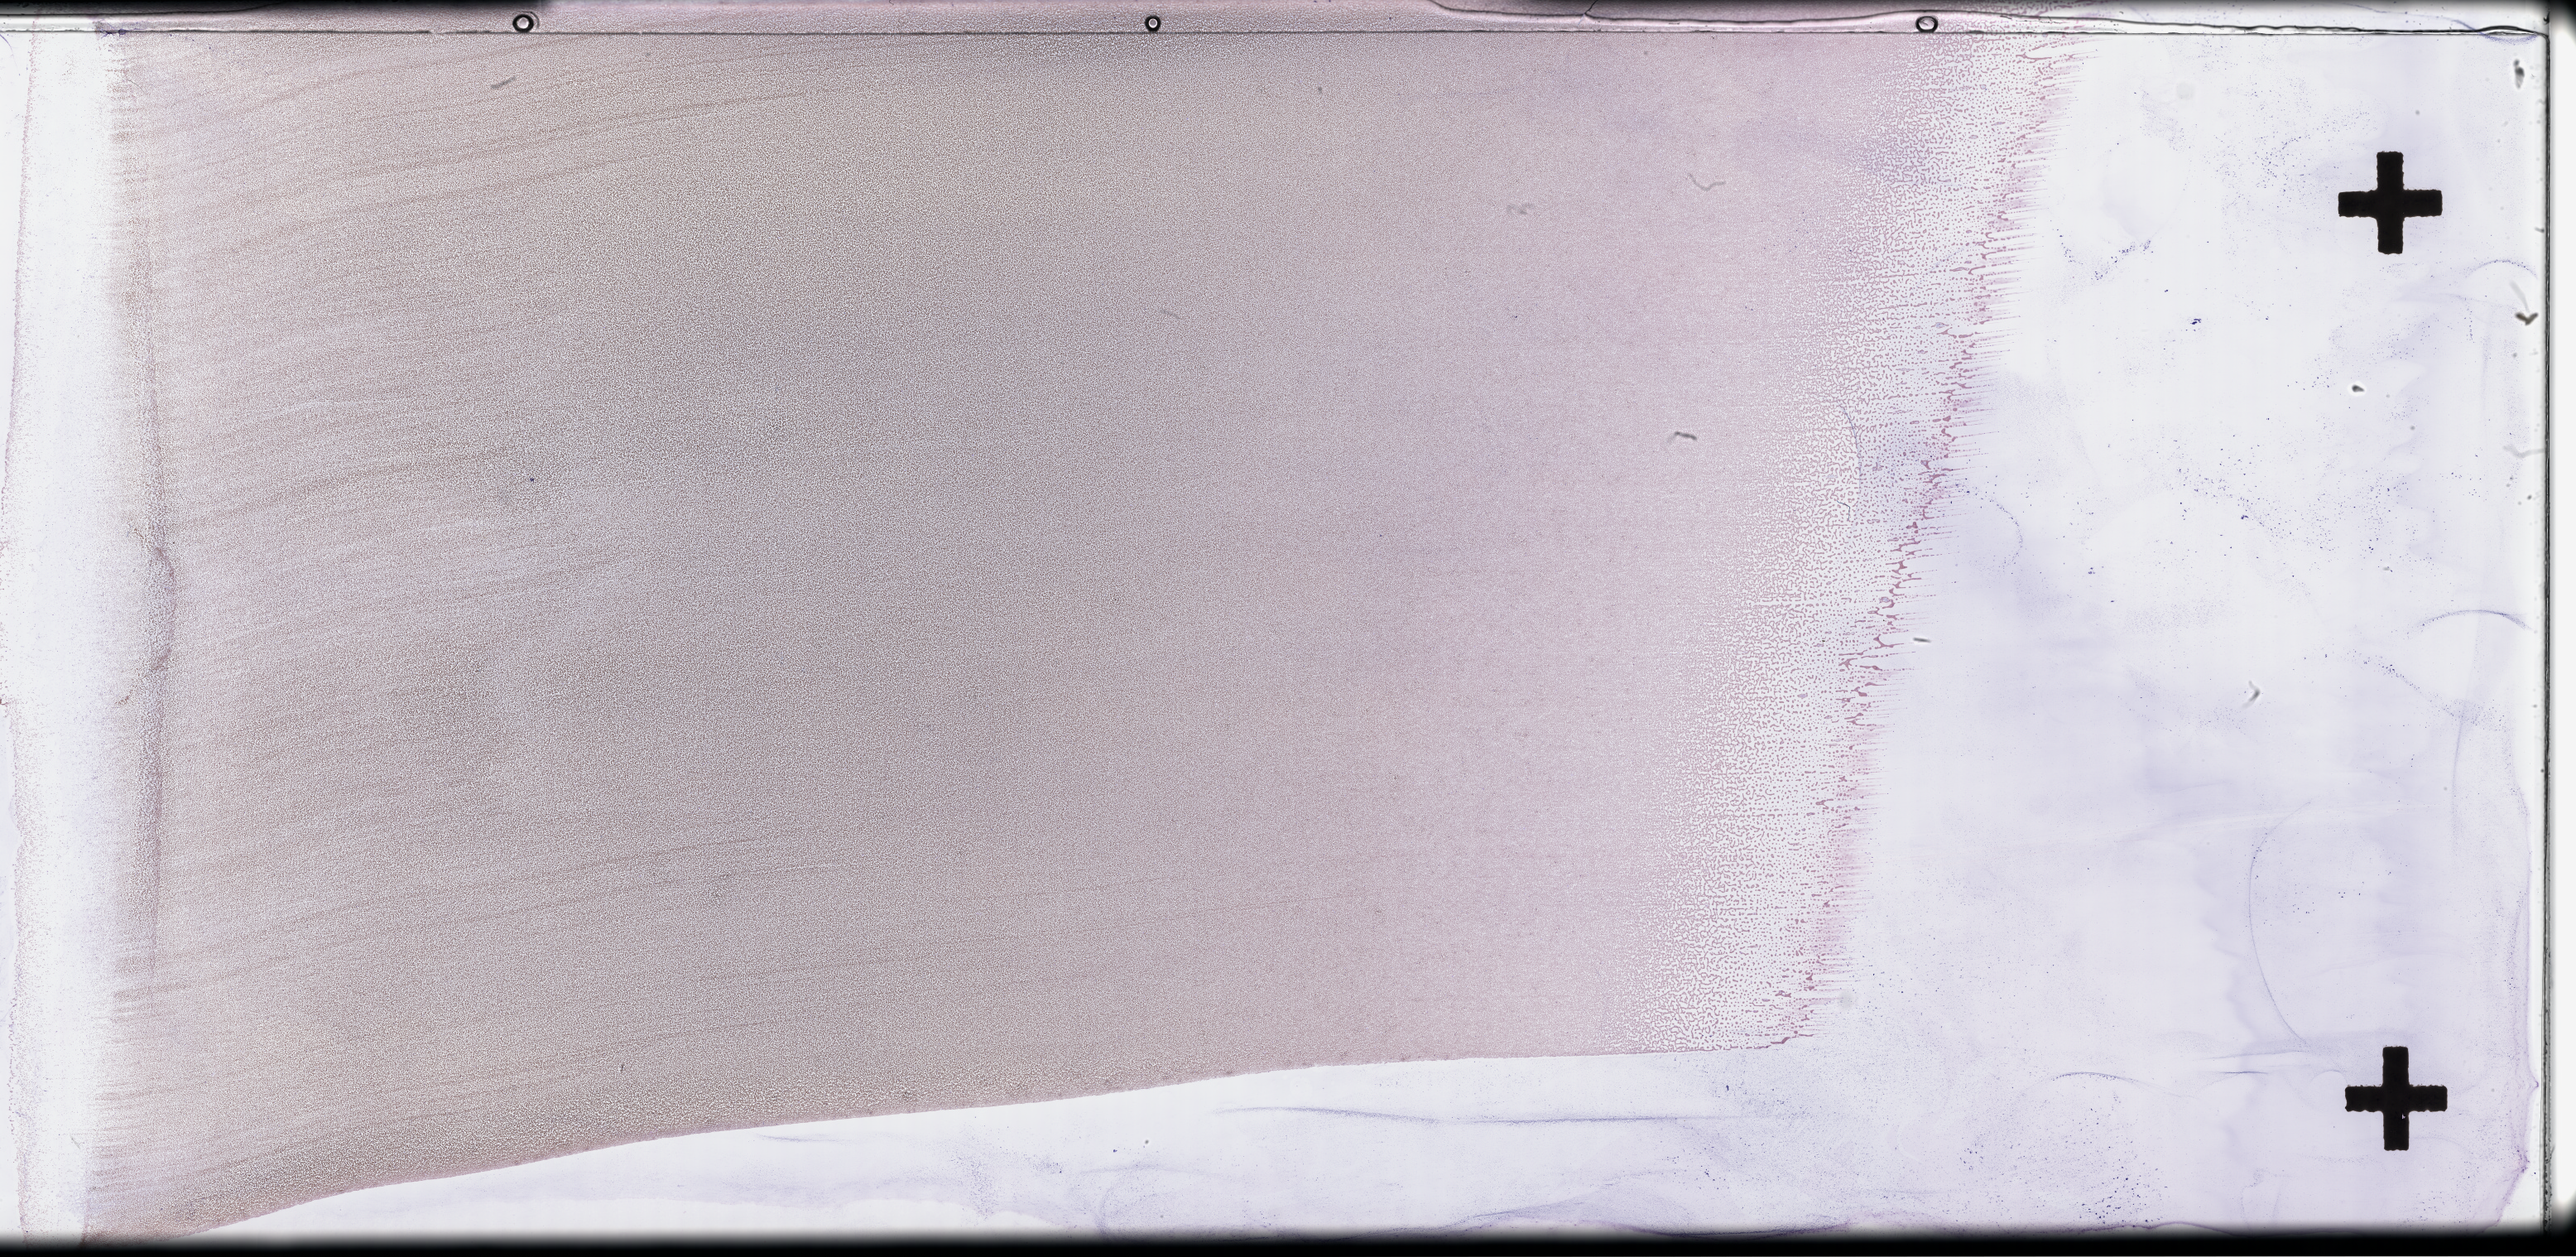
Wright–Giemsa-stained whole blood smear, whole-slide image — a low-resolution overview of the entire scanned area, about 50.3 x 24.5 mm, EDTA-anticoagulated smear, collected at baseline (before treatment). Male patient.
- from a patient with: Plasma Cell Myeloma